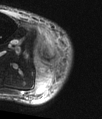
MRI of an extremity soft-tissue mass, one axial slice; position 14 of 48 along the scan axis; T2-weighted fat-saturated; MR volume resampled by the dataset authors to the PET/CT grid (not the native acquisition matrix); 3.27 mm slice thickness; 102 × 119 image matrix. Male patient. From the clinical record (not read from this slice): histological type: pleiomorphic liposarcoma; grade: high; site of the primary tumour: right calf.
Structures marked on this image (expert contour drawn on MRI and transferred to this co-registered scan by the dataset authors):
- gross tumour volume including surrounding oedema: bounding box (x1, y1, x2, y2) in pixels: (33, 39, 61, 81)
- gross tumour volume (mass): (48, 58, 50, 61)